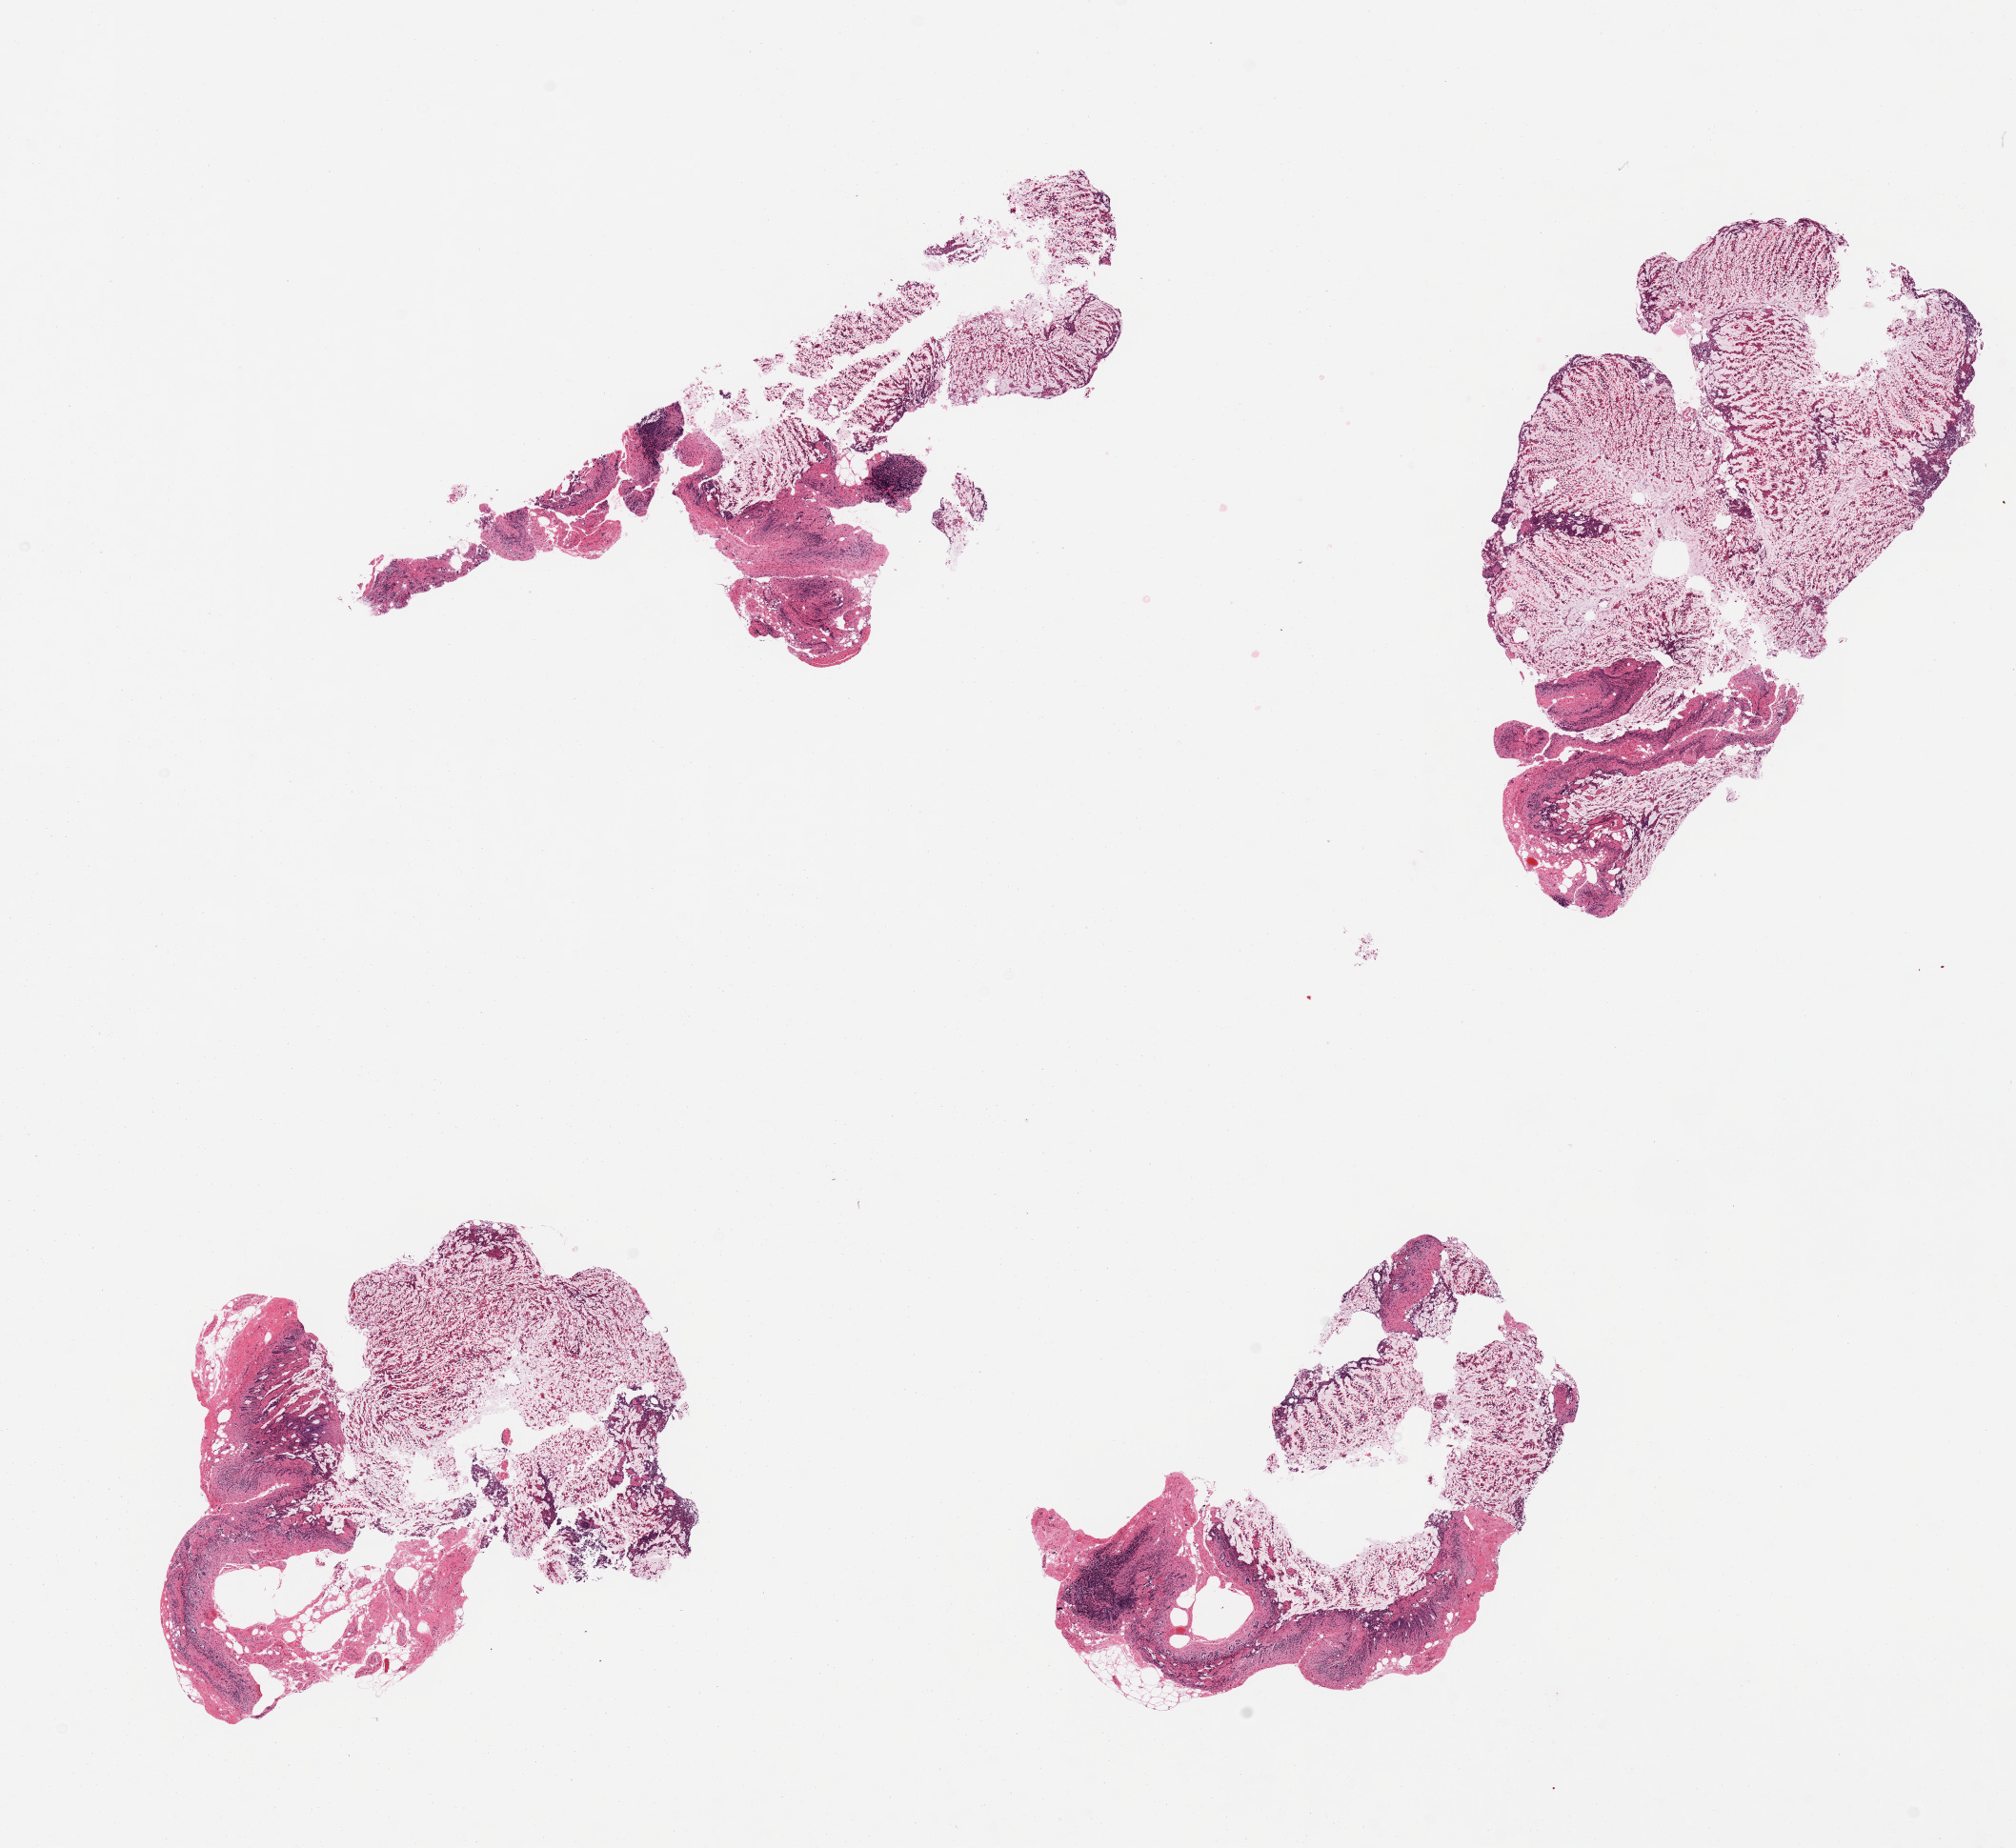
Hematoxylin and eosin (H&E) whole-slide image, shown as a low-resolution overview of the whole scanned area (about 16.7 x 15.3 mm), PAXgene-fixed paraffin-embedded (PFPE) section, sampled site (target tissue): ileum, donor tissue sample. Male donor.
- review note (as recorded): 4 pieces, fragments of autolyzed mucosa and mucus/cellular debris with only rare lymphoid aggregate